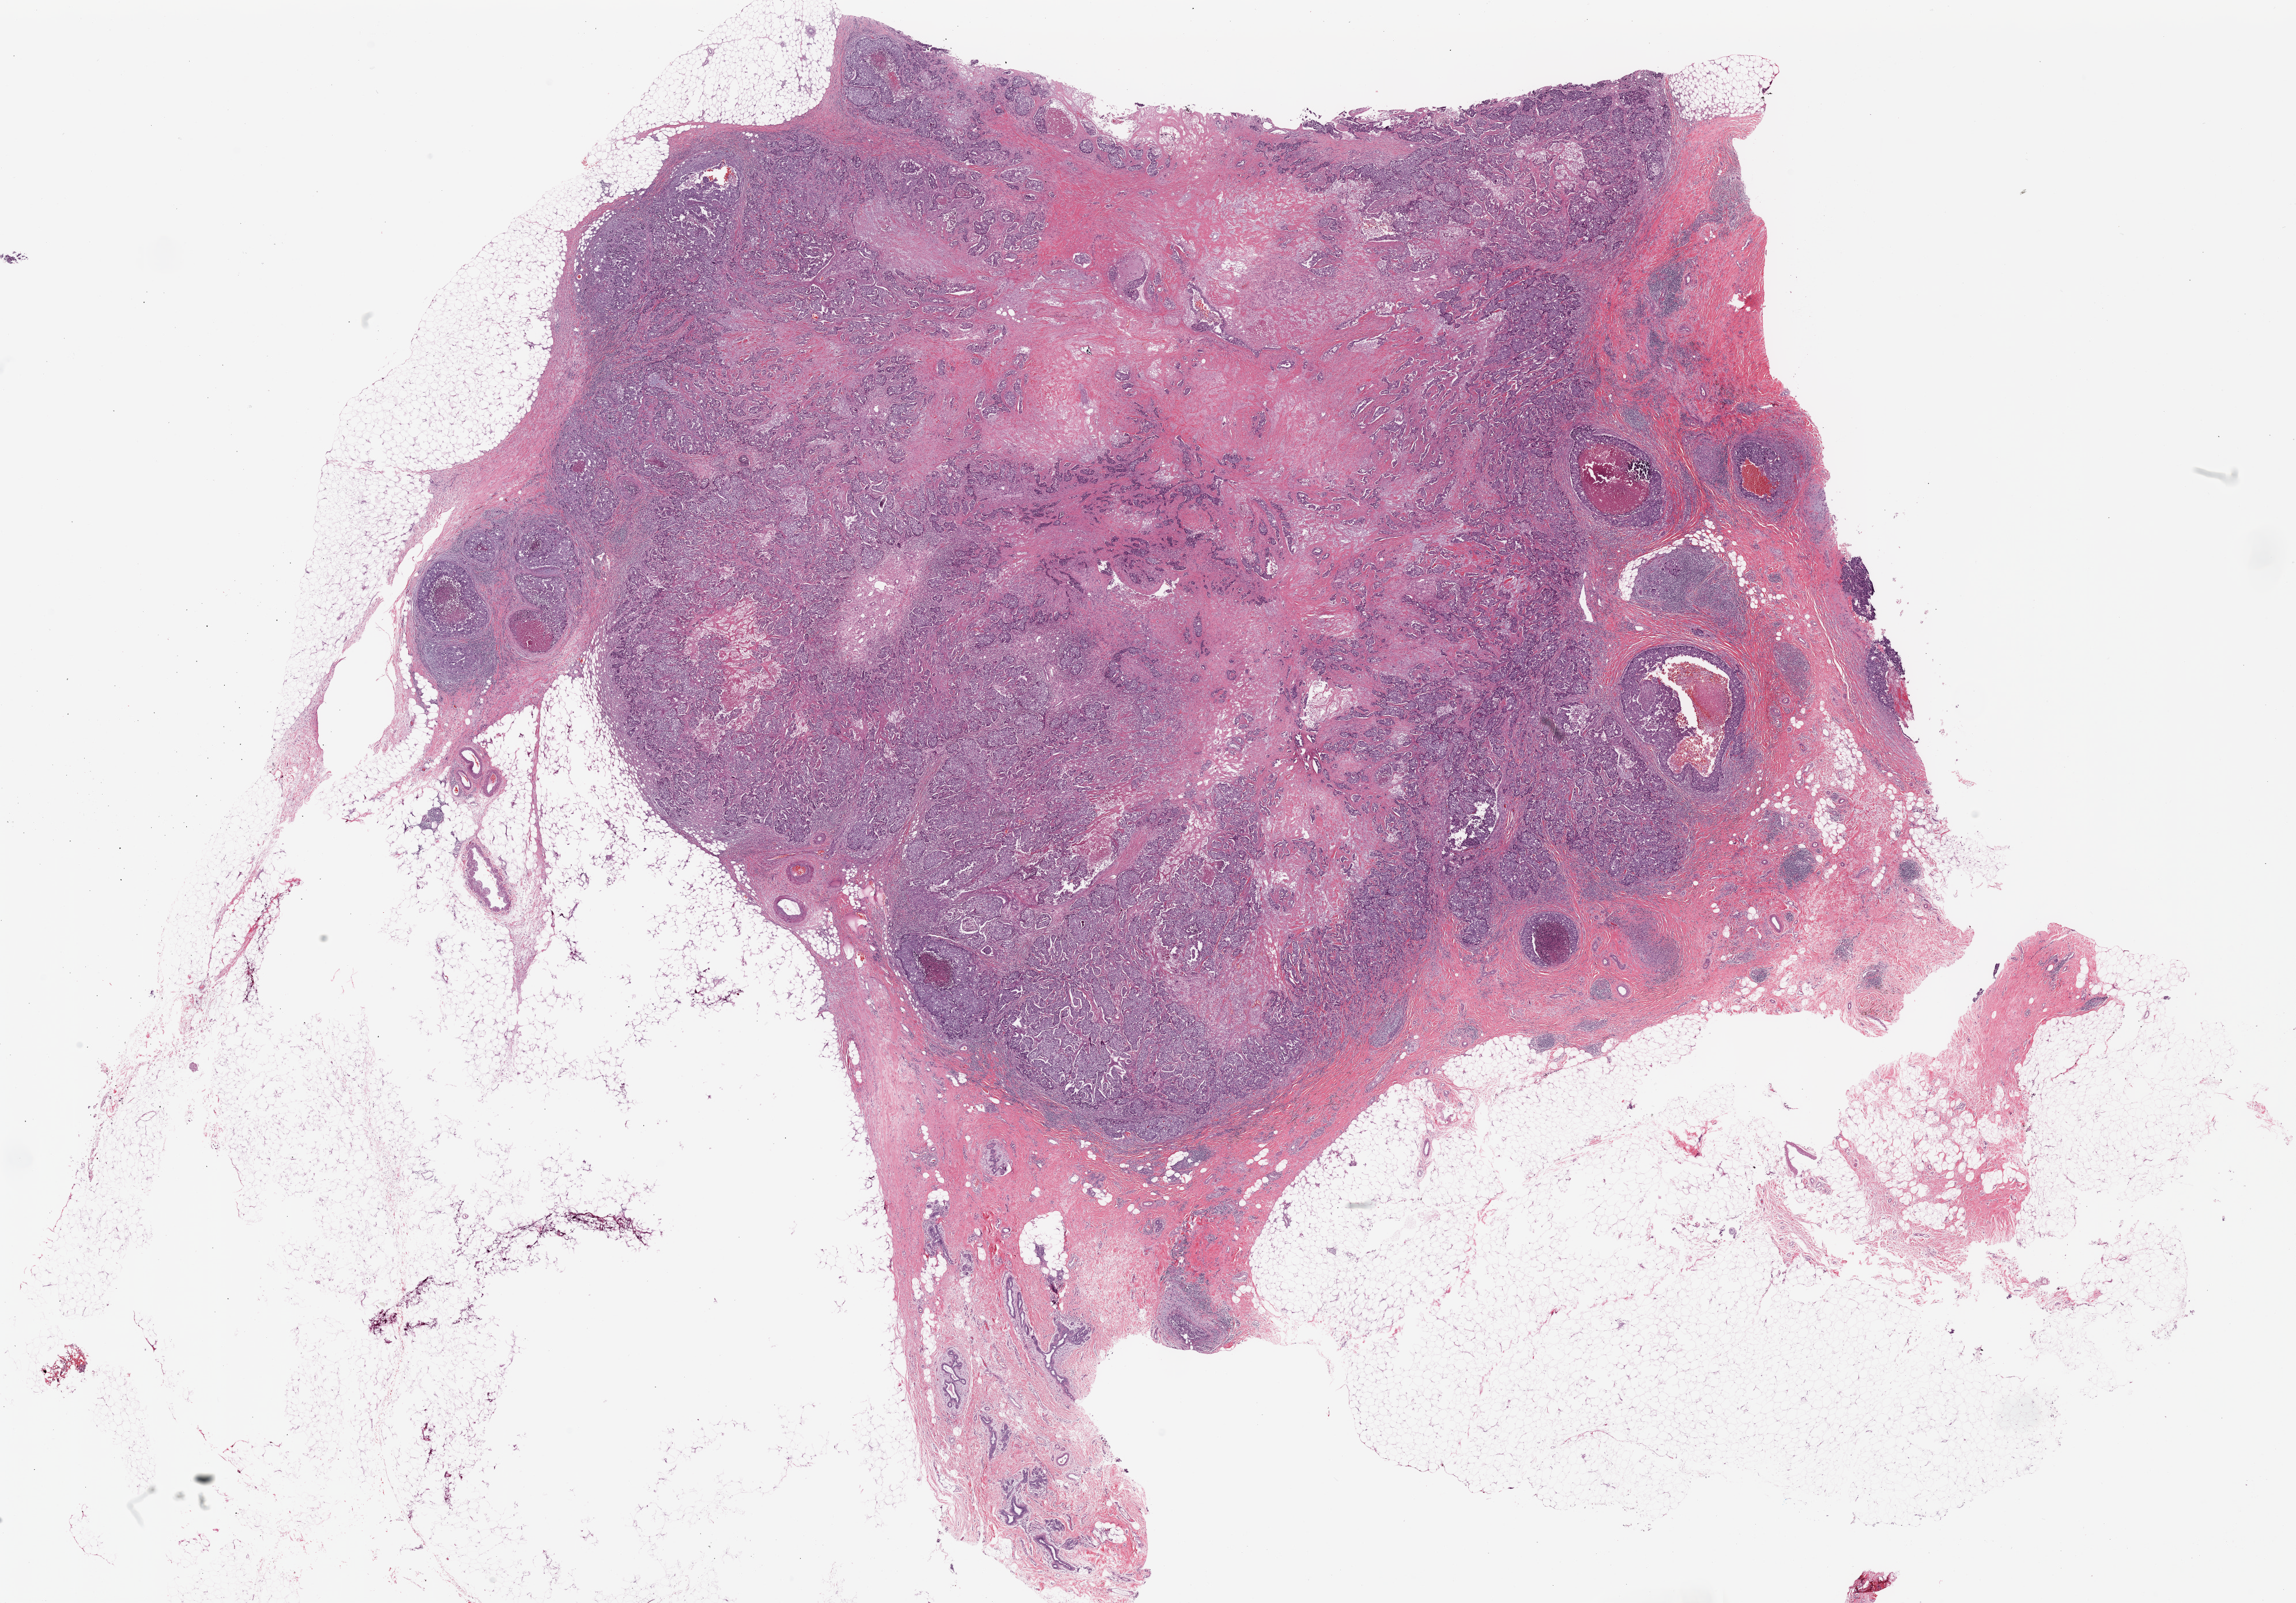
H&E whole-slide image — whole scanned area (about 31.8 x 22.2 mm, acquisition: 20x scan) shown as a low-resolution overview, formalin-fixed paraffin-embedded (FFPE) diagnostic section, sample: primary tumour, breast. Female, age 59 years at initial diagnosis.
Pathologic diagnosis: Infiltrating duct carcinoma, NOS. AJCC pathologic stage: IIIA. Lymph nodes positive (case pathology): 7 of 26 examined.